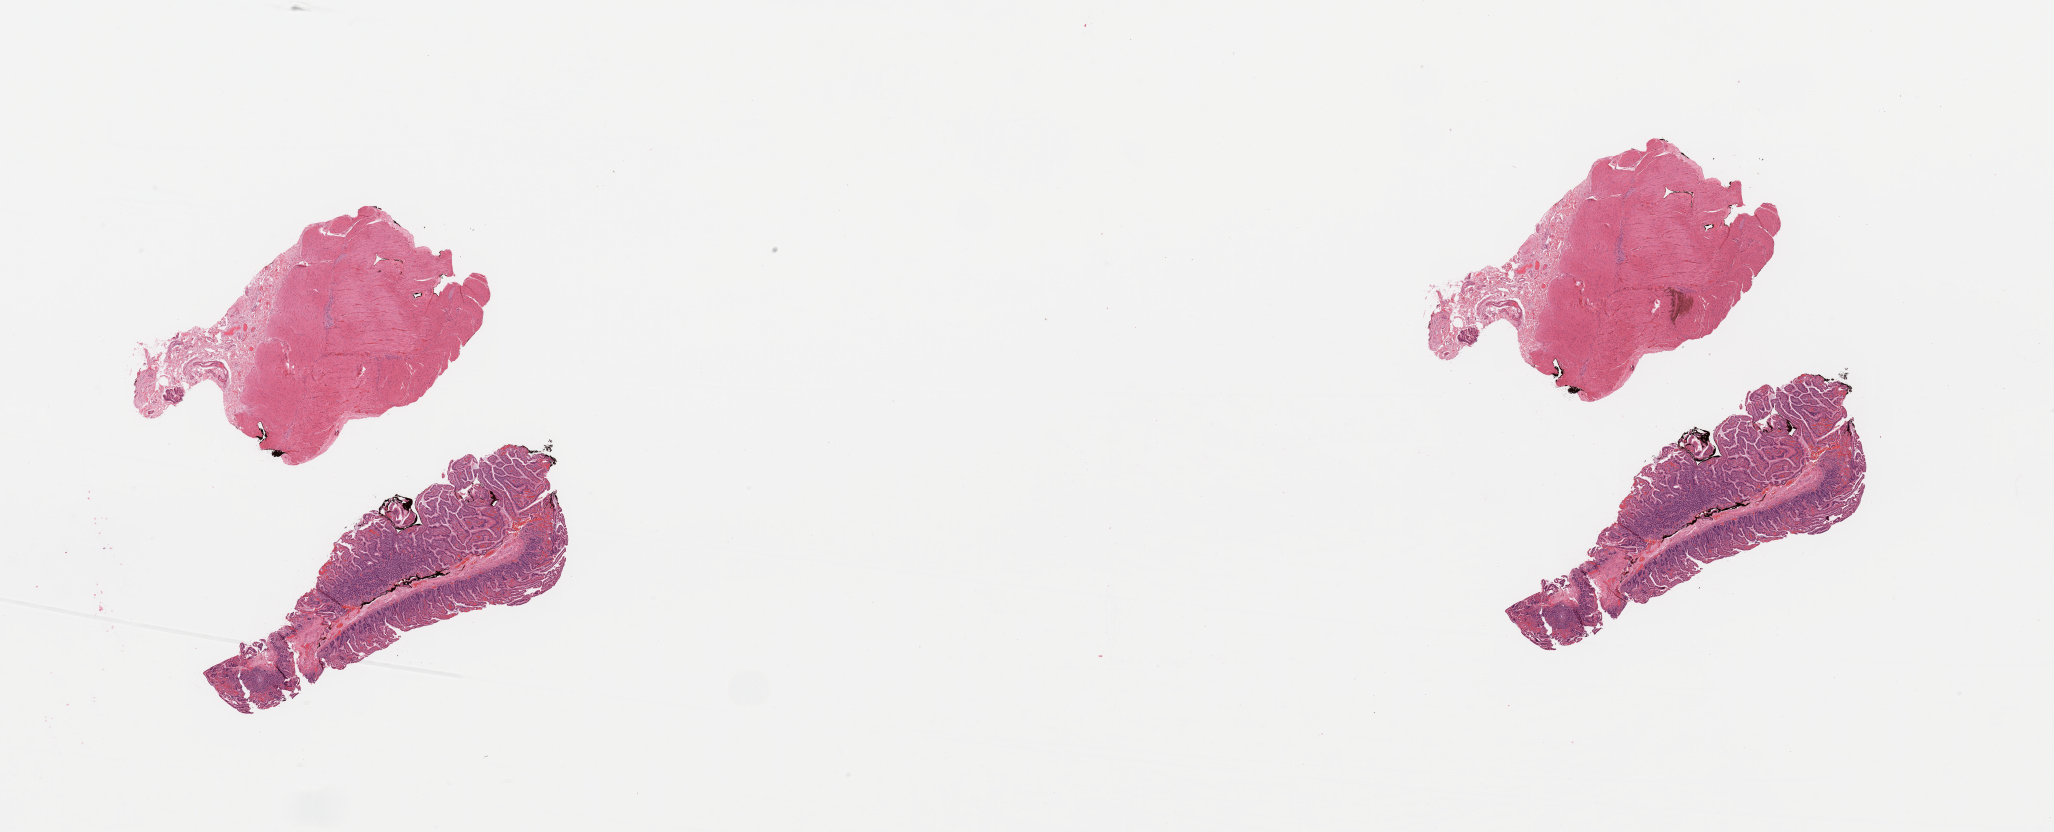
Digitized H&E-stained tissue section (whole slide) — a low-resolution overview of the entire scanned area, about 32.5 x 13.2 mm (from a 20x scan). Normal (non-tumour) tissue sample, sampled site: pancreas. 66-year-old male patient.
This section: normal (non-tumour) tissue from the same patient. Patient diagnosis: Infiltrating duct carcinoma, NOS.